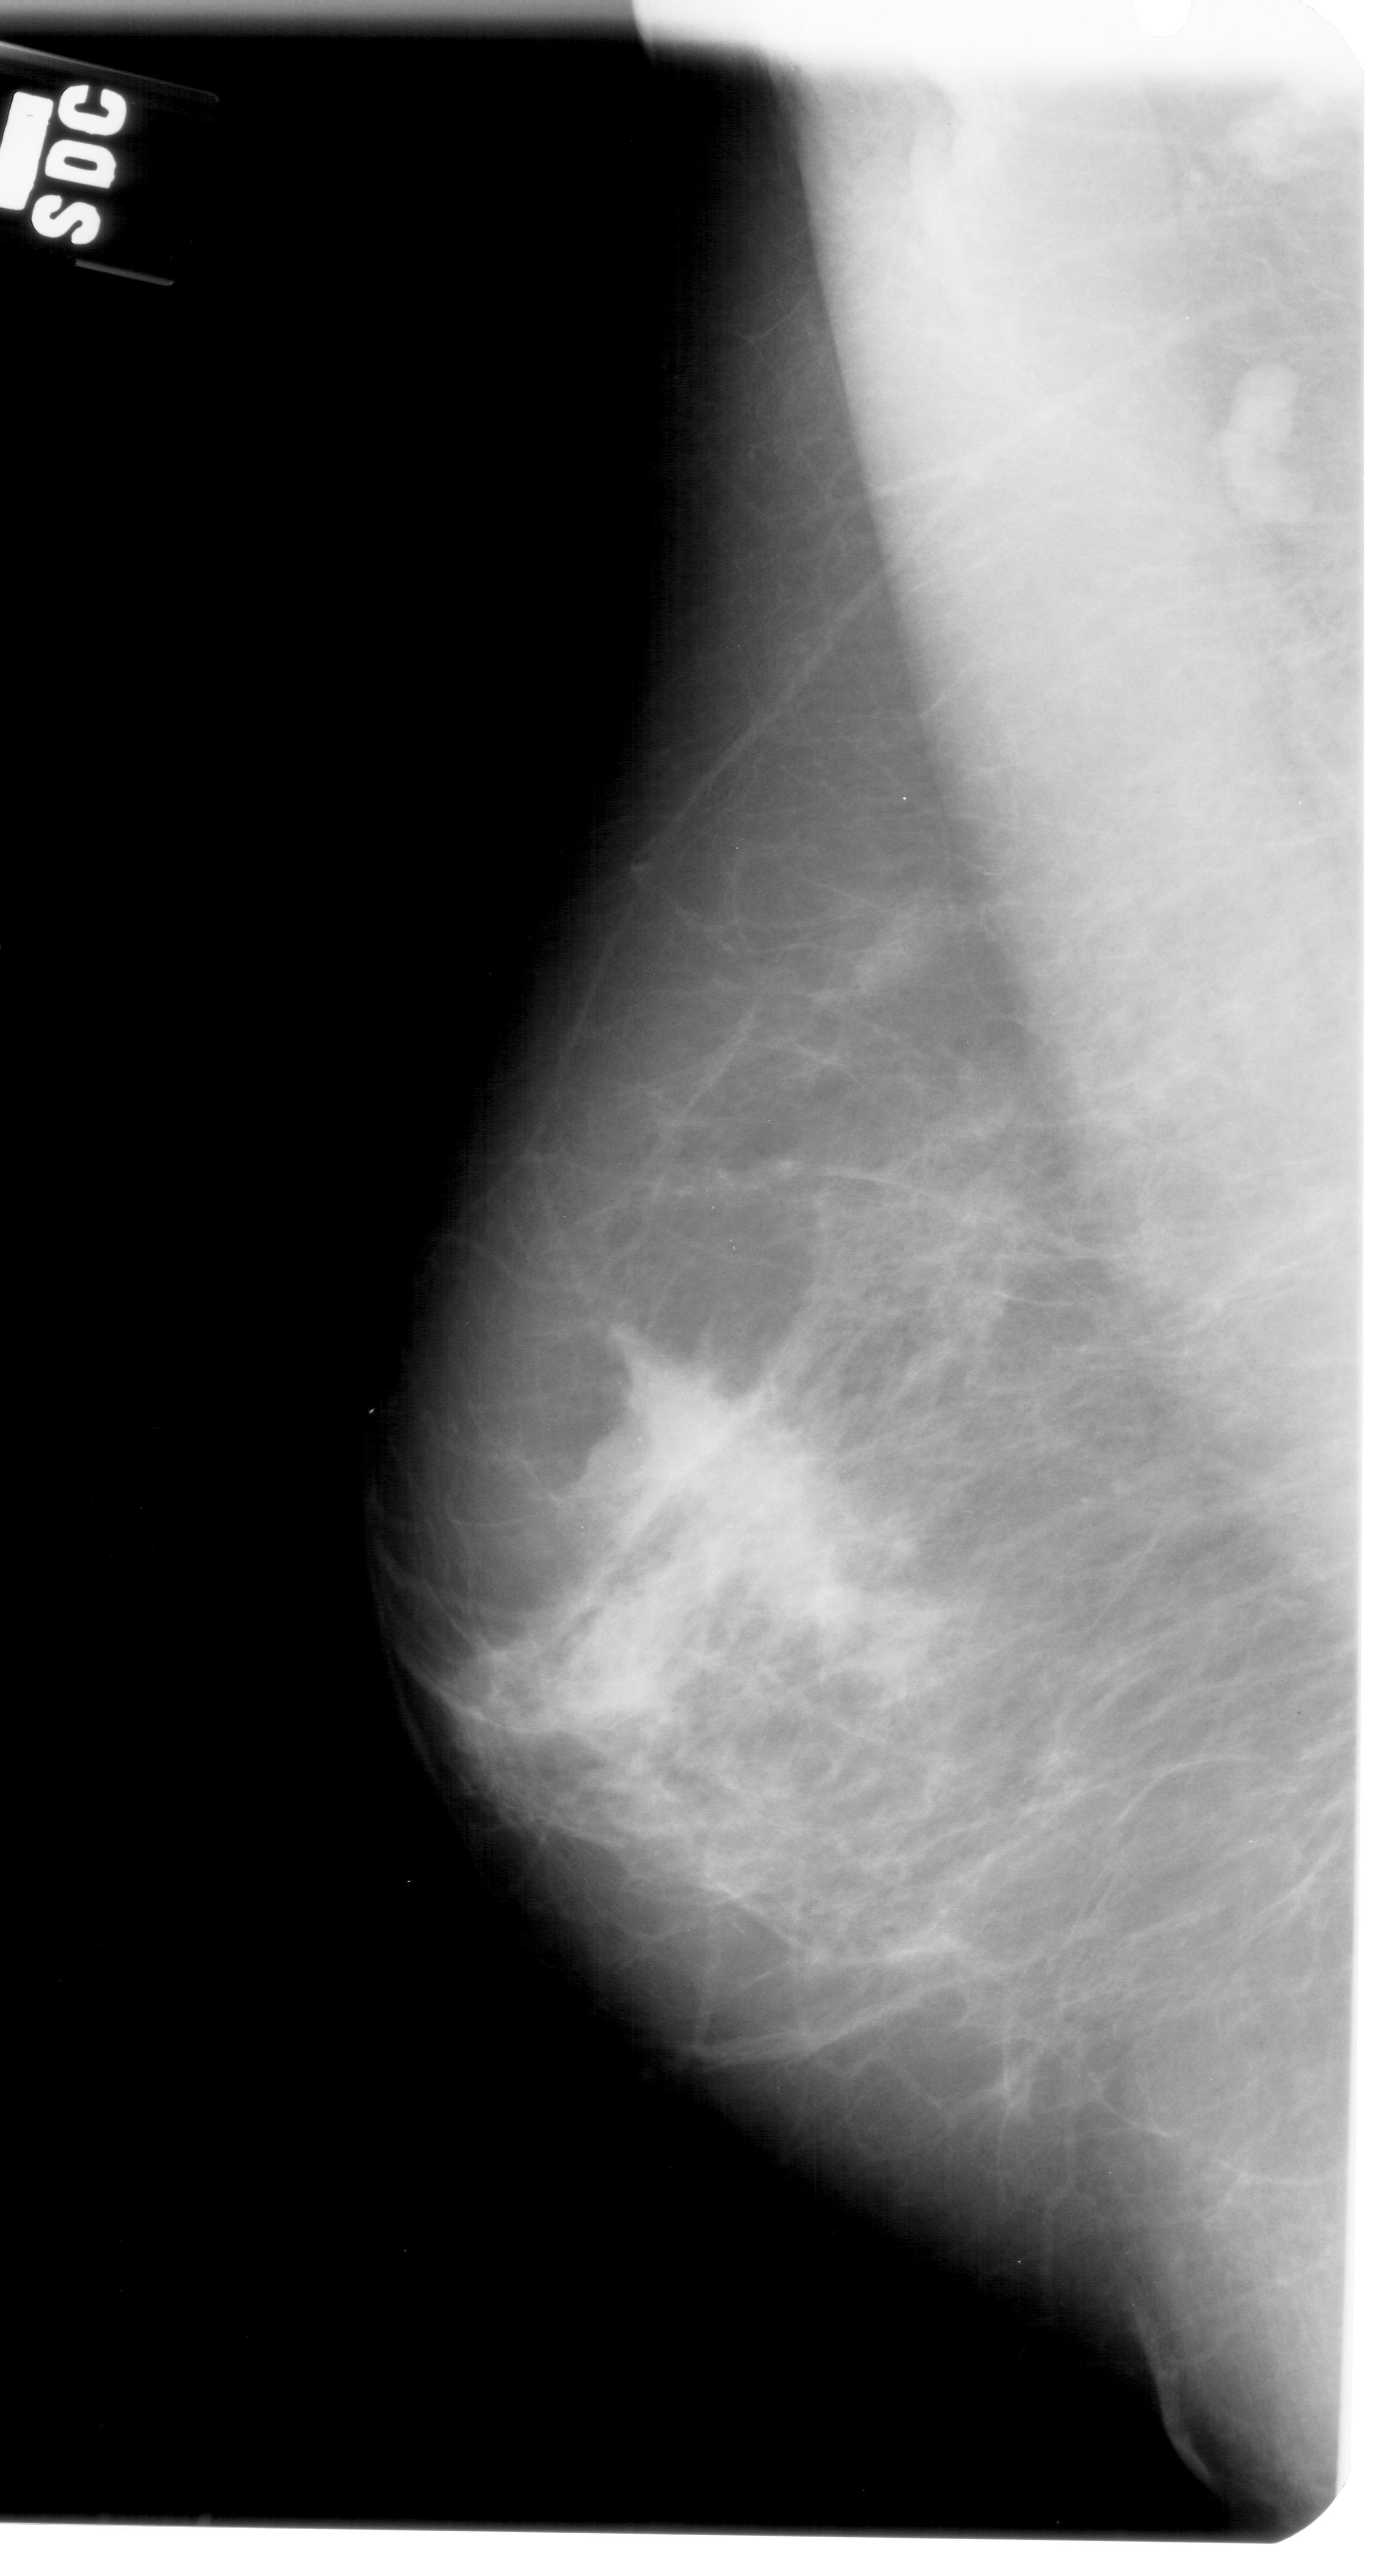
Digitized screen-film mammogram; left breast; mediolateral oblique (MLO) view; BI-RADS breast density category 2 (scale 1–4).
Abnormality record for this image: mass, shape irregular, margins ill defined; BI-RADS assessment category 4; pathology (as recorded): malignant.